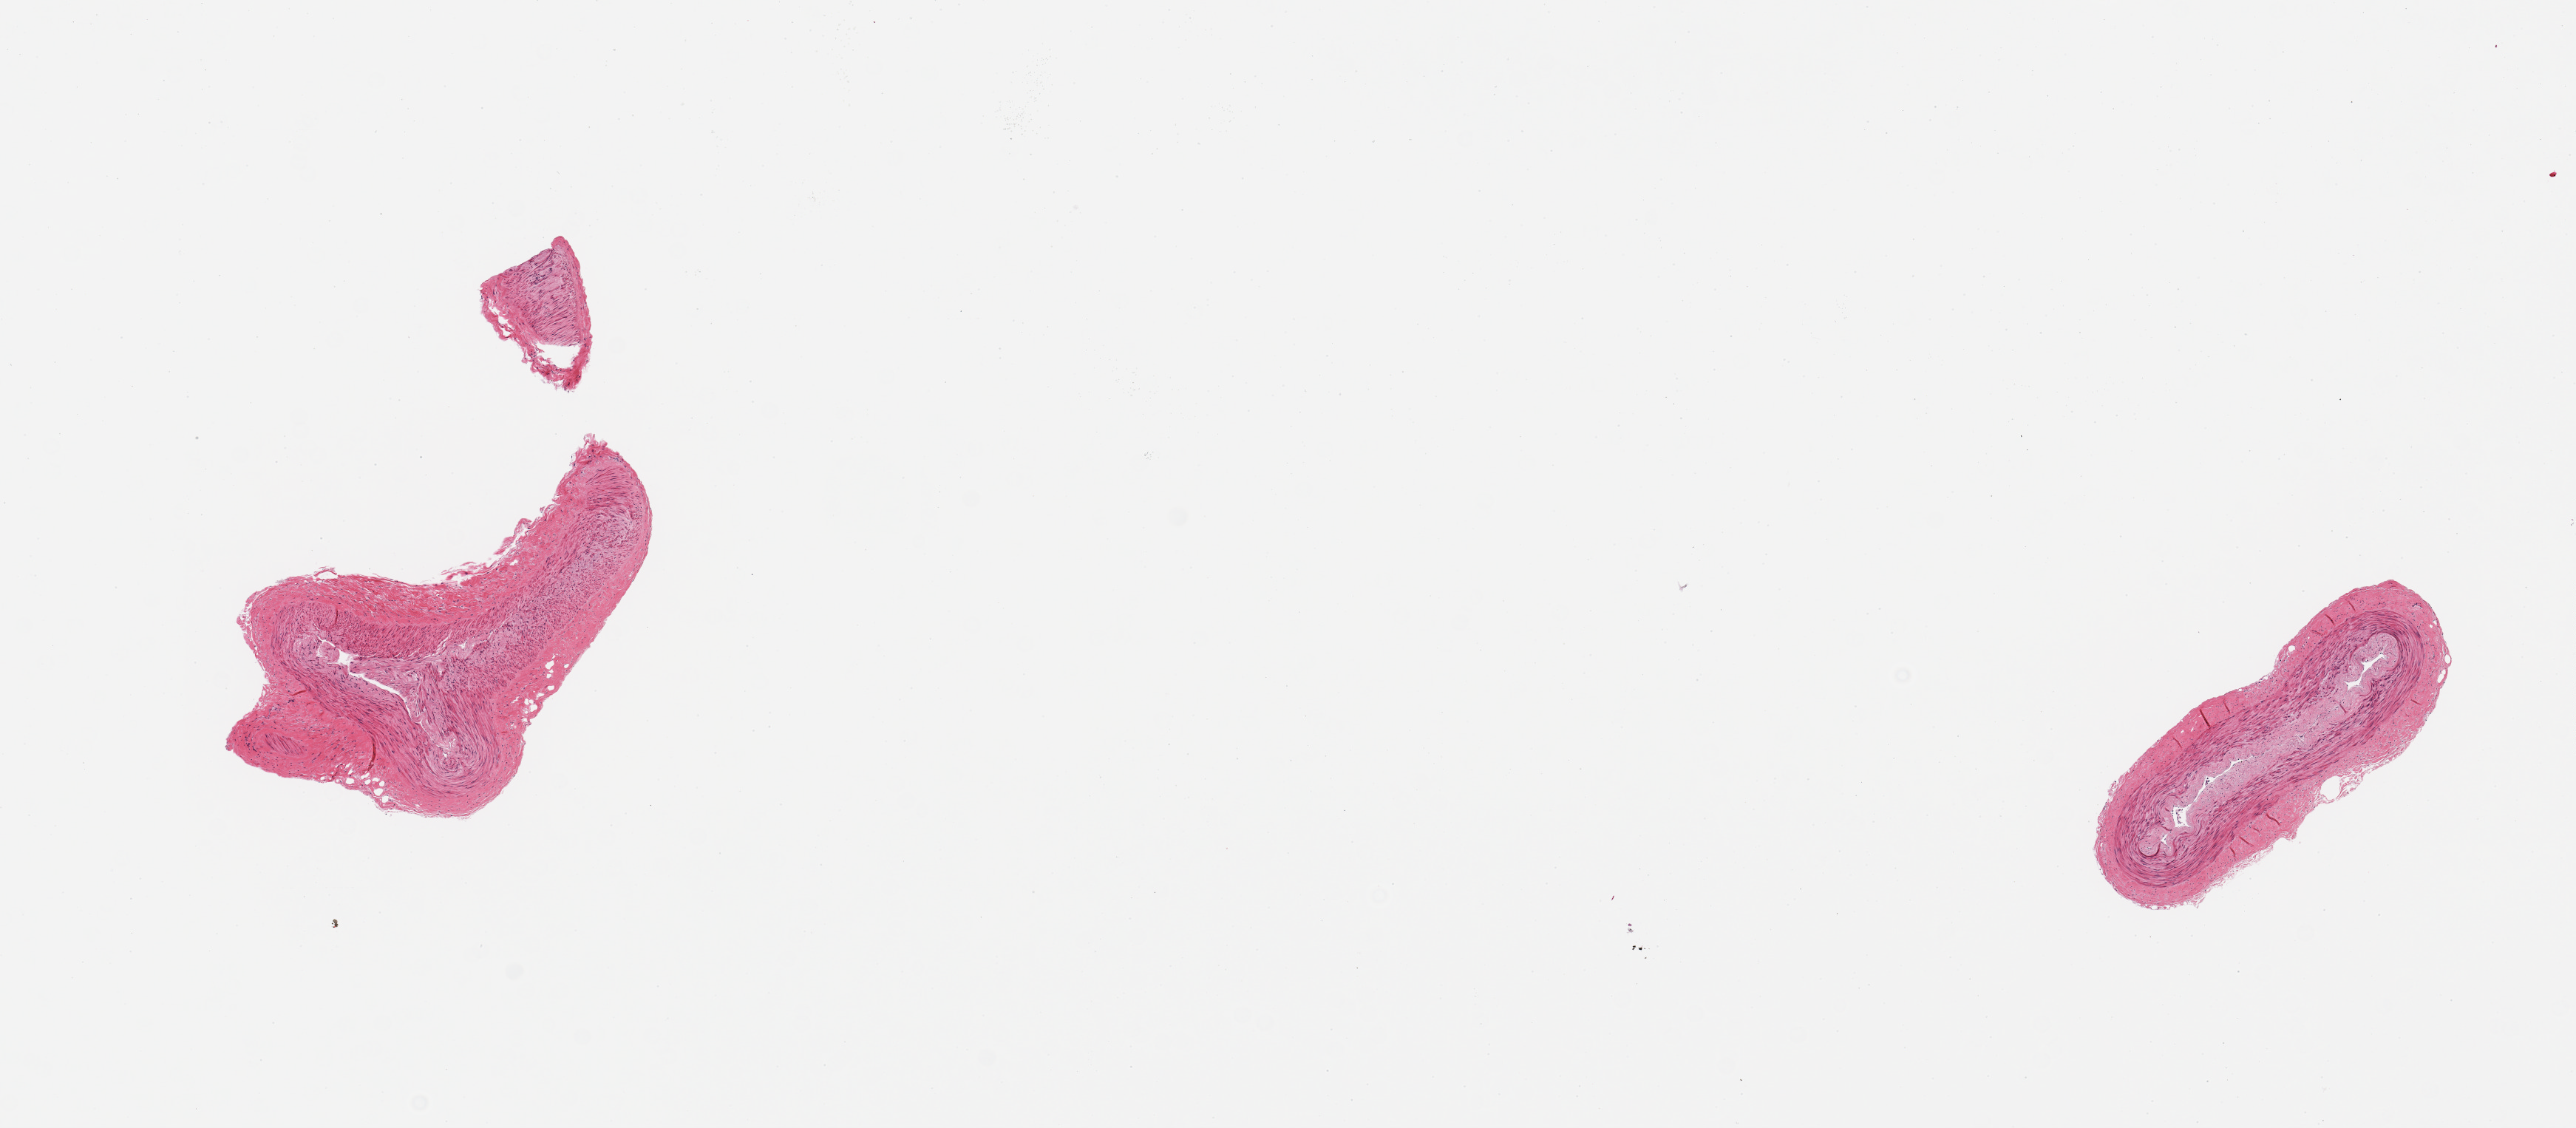
Digitized H&E-stained section, shown as a low-resolution overview of the whole scanned area (about 13.8 x 6.0 mm); PAXgene-fixed, paraffin-embedded tissue; section of tibial artery (target tissue); donor tissue sample. Donor sex: female.
Reviewer comment on this tissue sample: 2 pieces; well trimmed, intimal thickening/mild plaque.